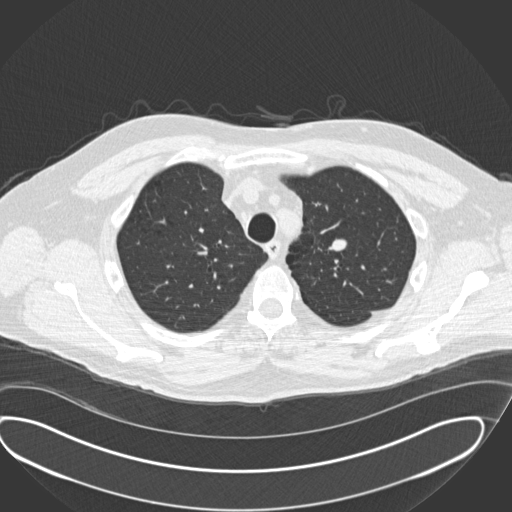
Chest CT (low-dose screening protocol), one axial image; second annual screen; lung window (W 1500 / L -600 HU); 120 kVp; slice 45 of 190 in the series. Male participant, aged 56 years at enrolment. Current smoker at enrolment.
• Expert reader's lesion annotation, bounding box <312,226,368,271> (left, top, right, bottom; pixels).
• No non-calcified nodule or mass ≥4 mm was recorded by the screening reader at this exam.
• Official screen result: negative screen, significant abnormalities not suspicious for lung cancer.
• Participant outcome: lung cancer diagnosed 520 days after this screen — neuroendocrine carcinoma, NOS, left upper lobe, well differentiated (G1), stage IA (AJCC 6th edition), 20 mm at pathology.